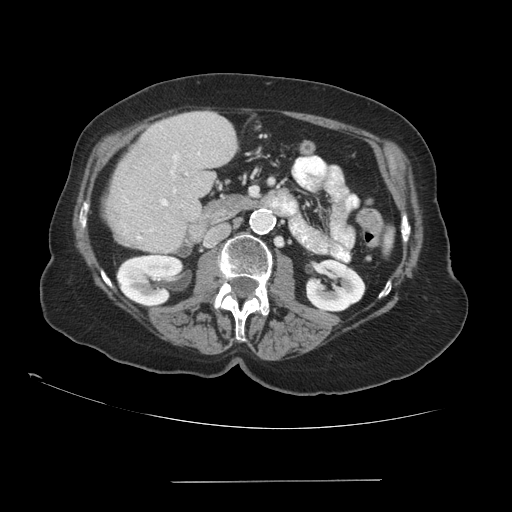
Contrast-enhanced abdominal CT (liver protocol), one axial slice. Position 35 of 89 along the scan axis. Reconstruction kernel STANDARD. 140 kVp. Soft-tissue window (W 400 / L 40 HU). 2.5 mm slice thickness. 512 × 512 image matrix, field of view 400 × 400 mm. From the clinical record (not read from this slice): diagnosis: hepatocellular carcinoma (patient treated with transarterial chemoembolisation; whether this scan precedes or follows treatment is not stated here); TNM stage (as recorded): Stage-IVA; Child-Pugh class: A; tumour differentiation: poorly differentiated.
Structures marked on this image (semi-automatically segmented with operator editing):
- liver parenchyma outside the tumour (the mass and vessels are separate outlines, so this box may not span the whole liver): box from (x=105, y=112) to (x=236, y=252) px
- liver vessels: (x=137, y=153)–(x=200, y=239)